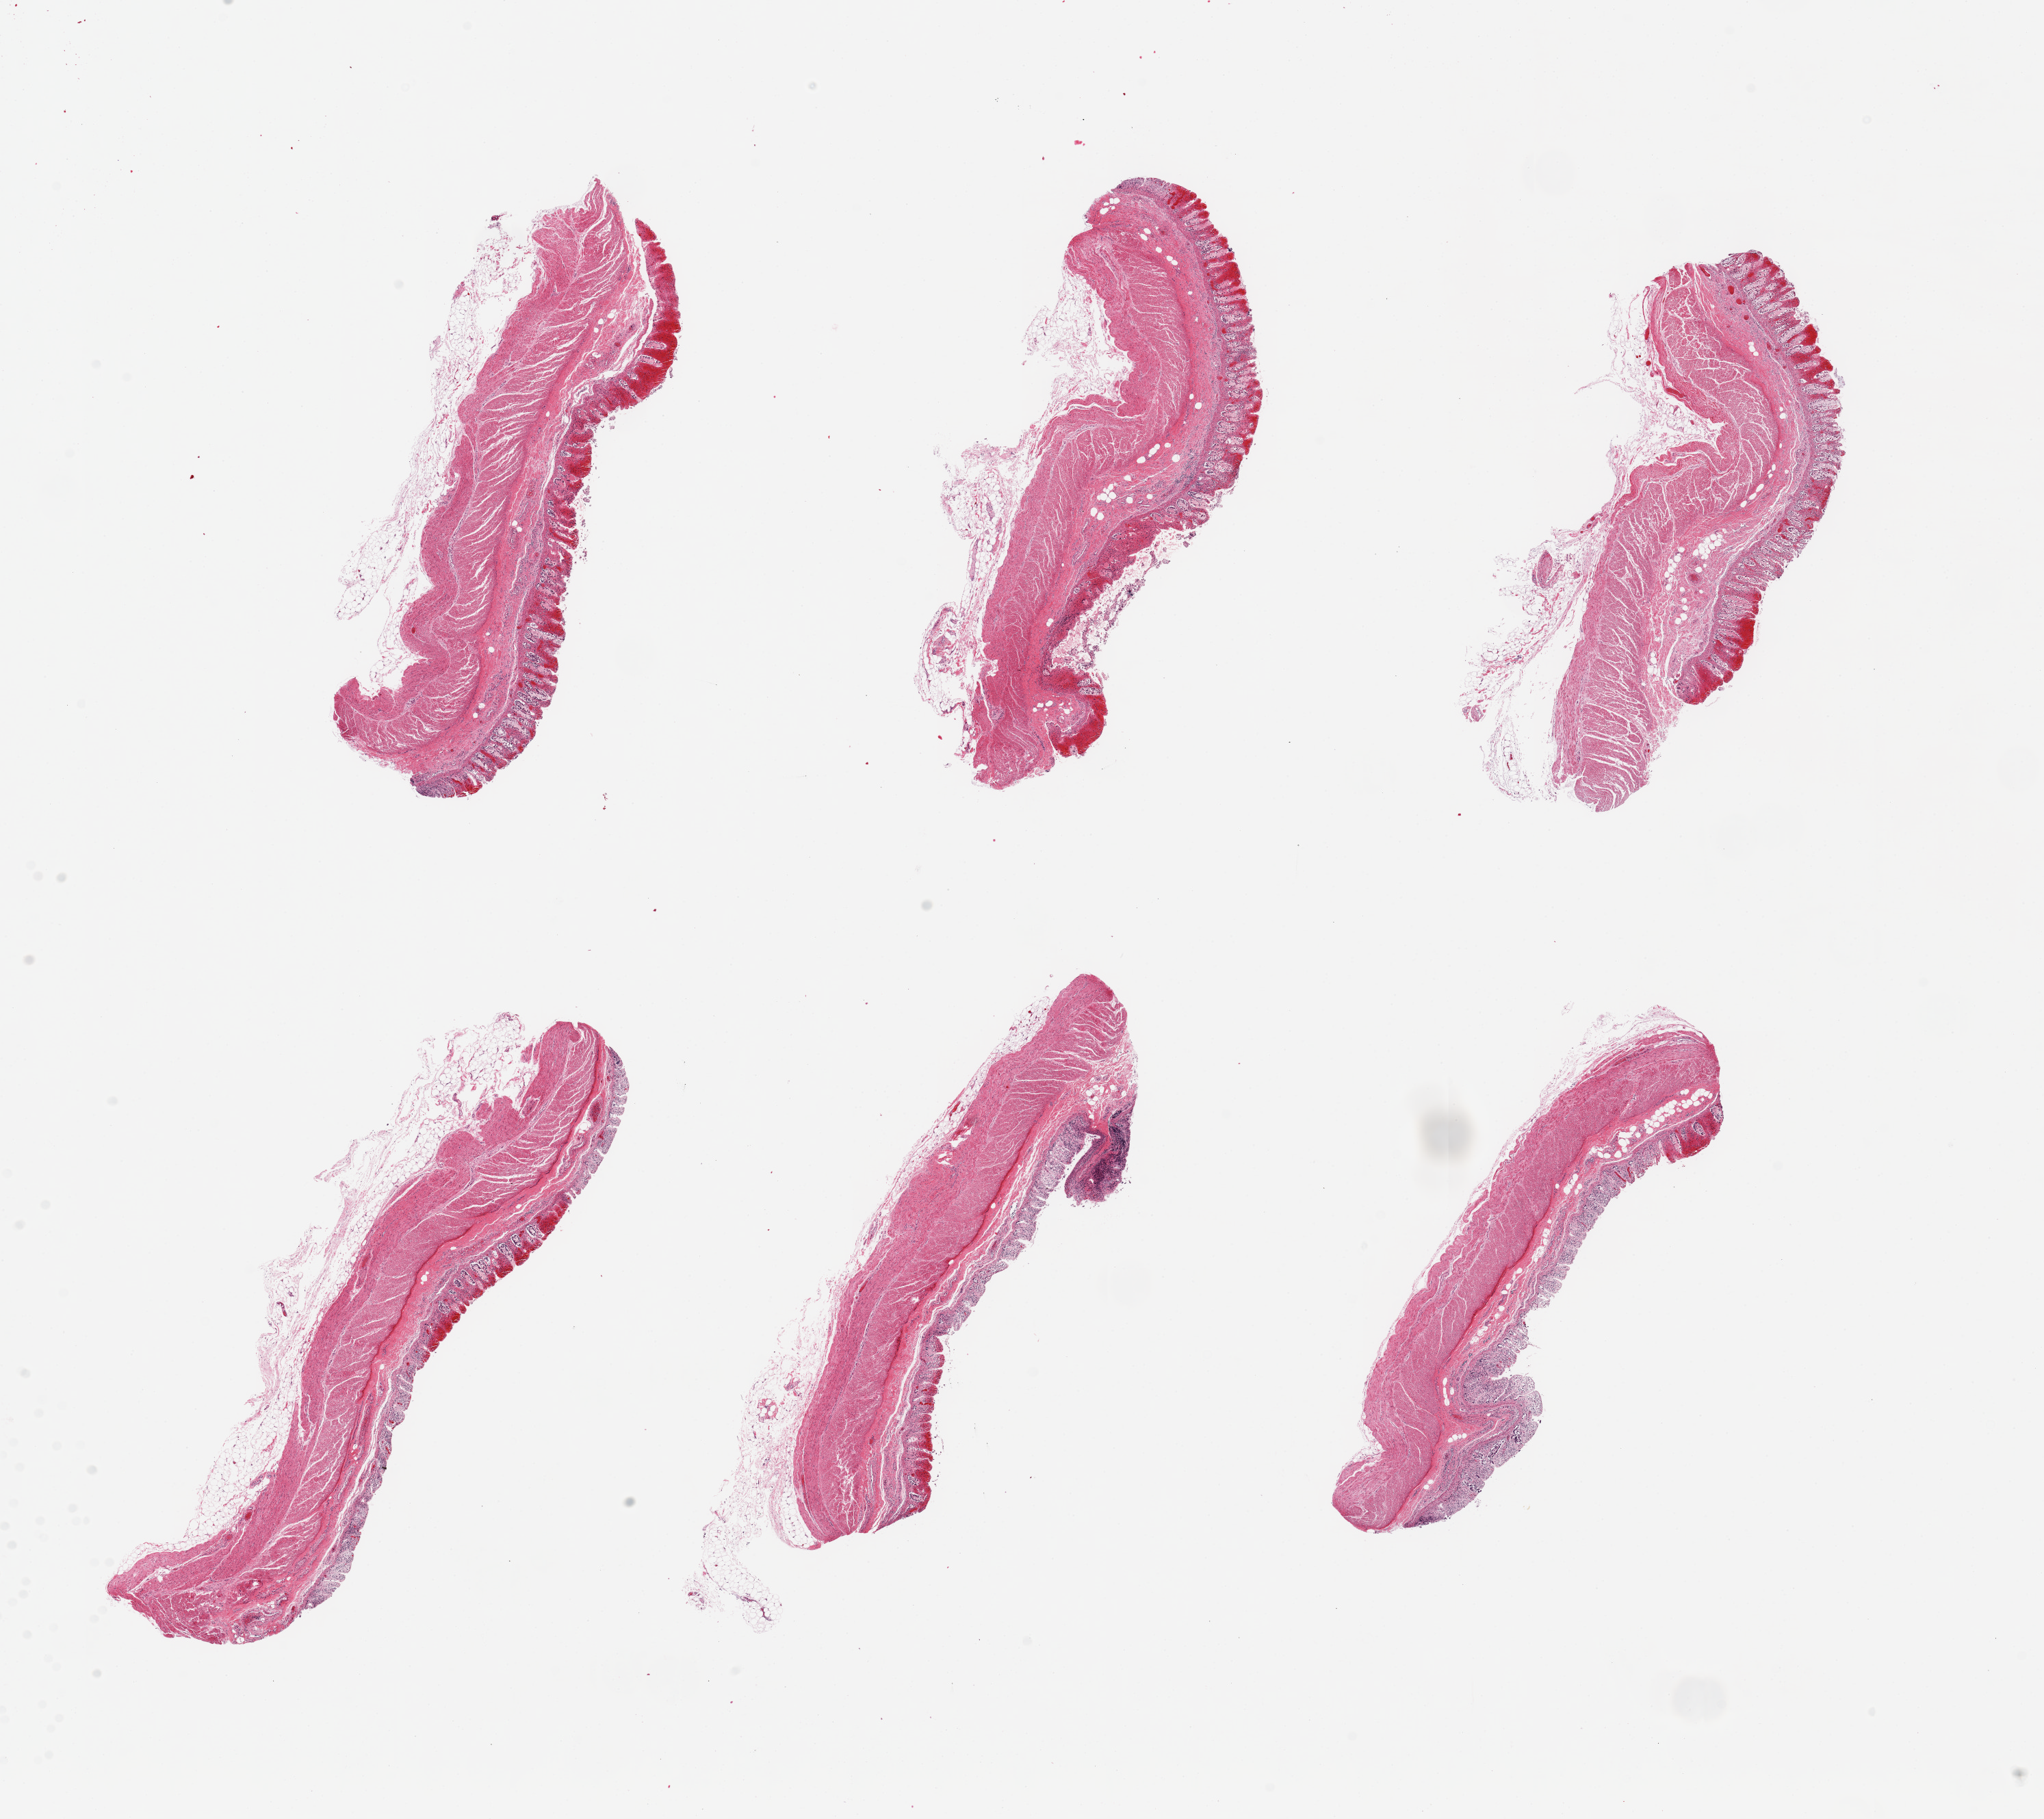
Whole-slide image, haematoxylin and eosin stain, whole scanned area (about 23.6 x 21.0 mm, slide scanned at 20x) shown as a low-resolution overview, PAXgene-fixed, paraffin-embedded tissue, target tissue: transverse colon, donor tissue sample.
Pathologist's review note for this sample: 6 pieces, up to 8.5x3mm; Mucosa=3; muscle = 2. Mucosal hemorrhagic infarcts (bowel infarcts by clinical history).